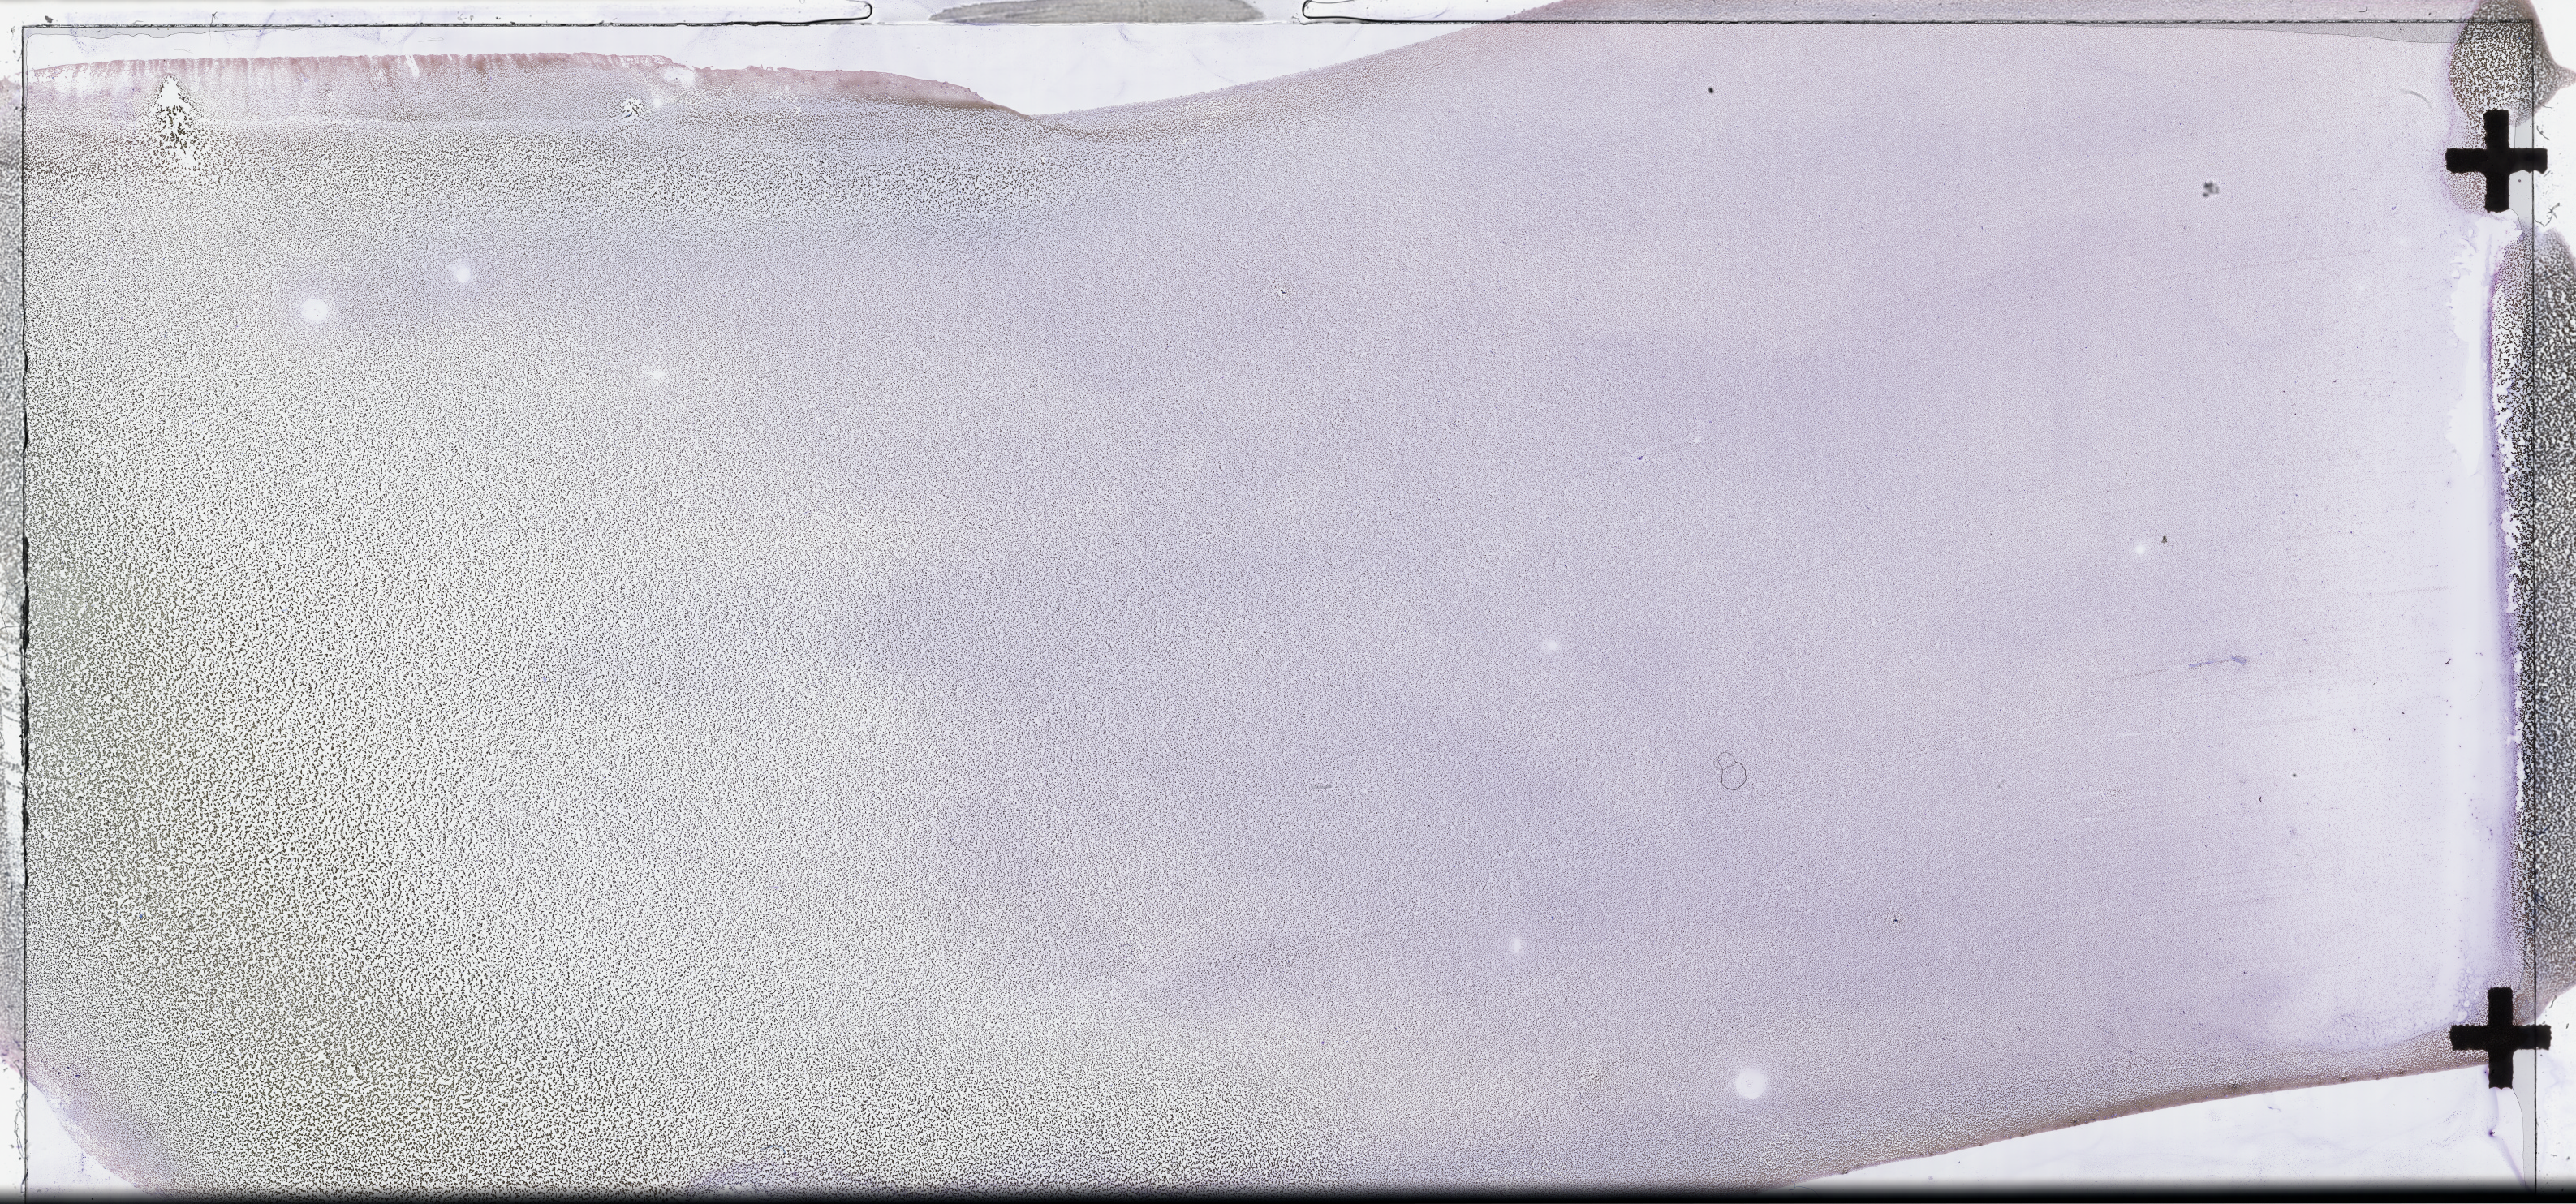
Whole-slide image of a bone marrow smear, Wright-Giemsa stain, low-resolution overview of the scanned area, about 51.3 x 24.0 mm; specimen time point: collected at baseline (before treatment). Male patient.
From a patient with: Plasma Cell Myeloma.